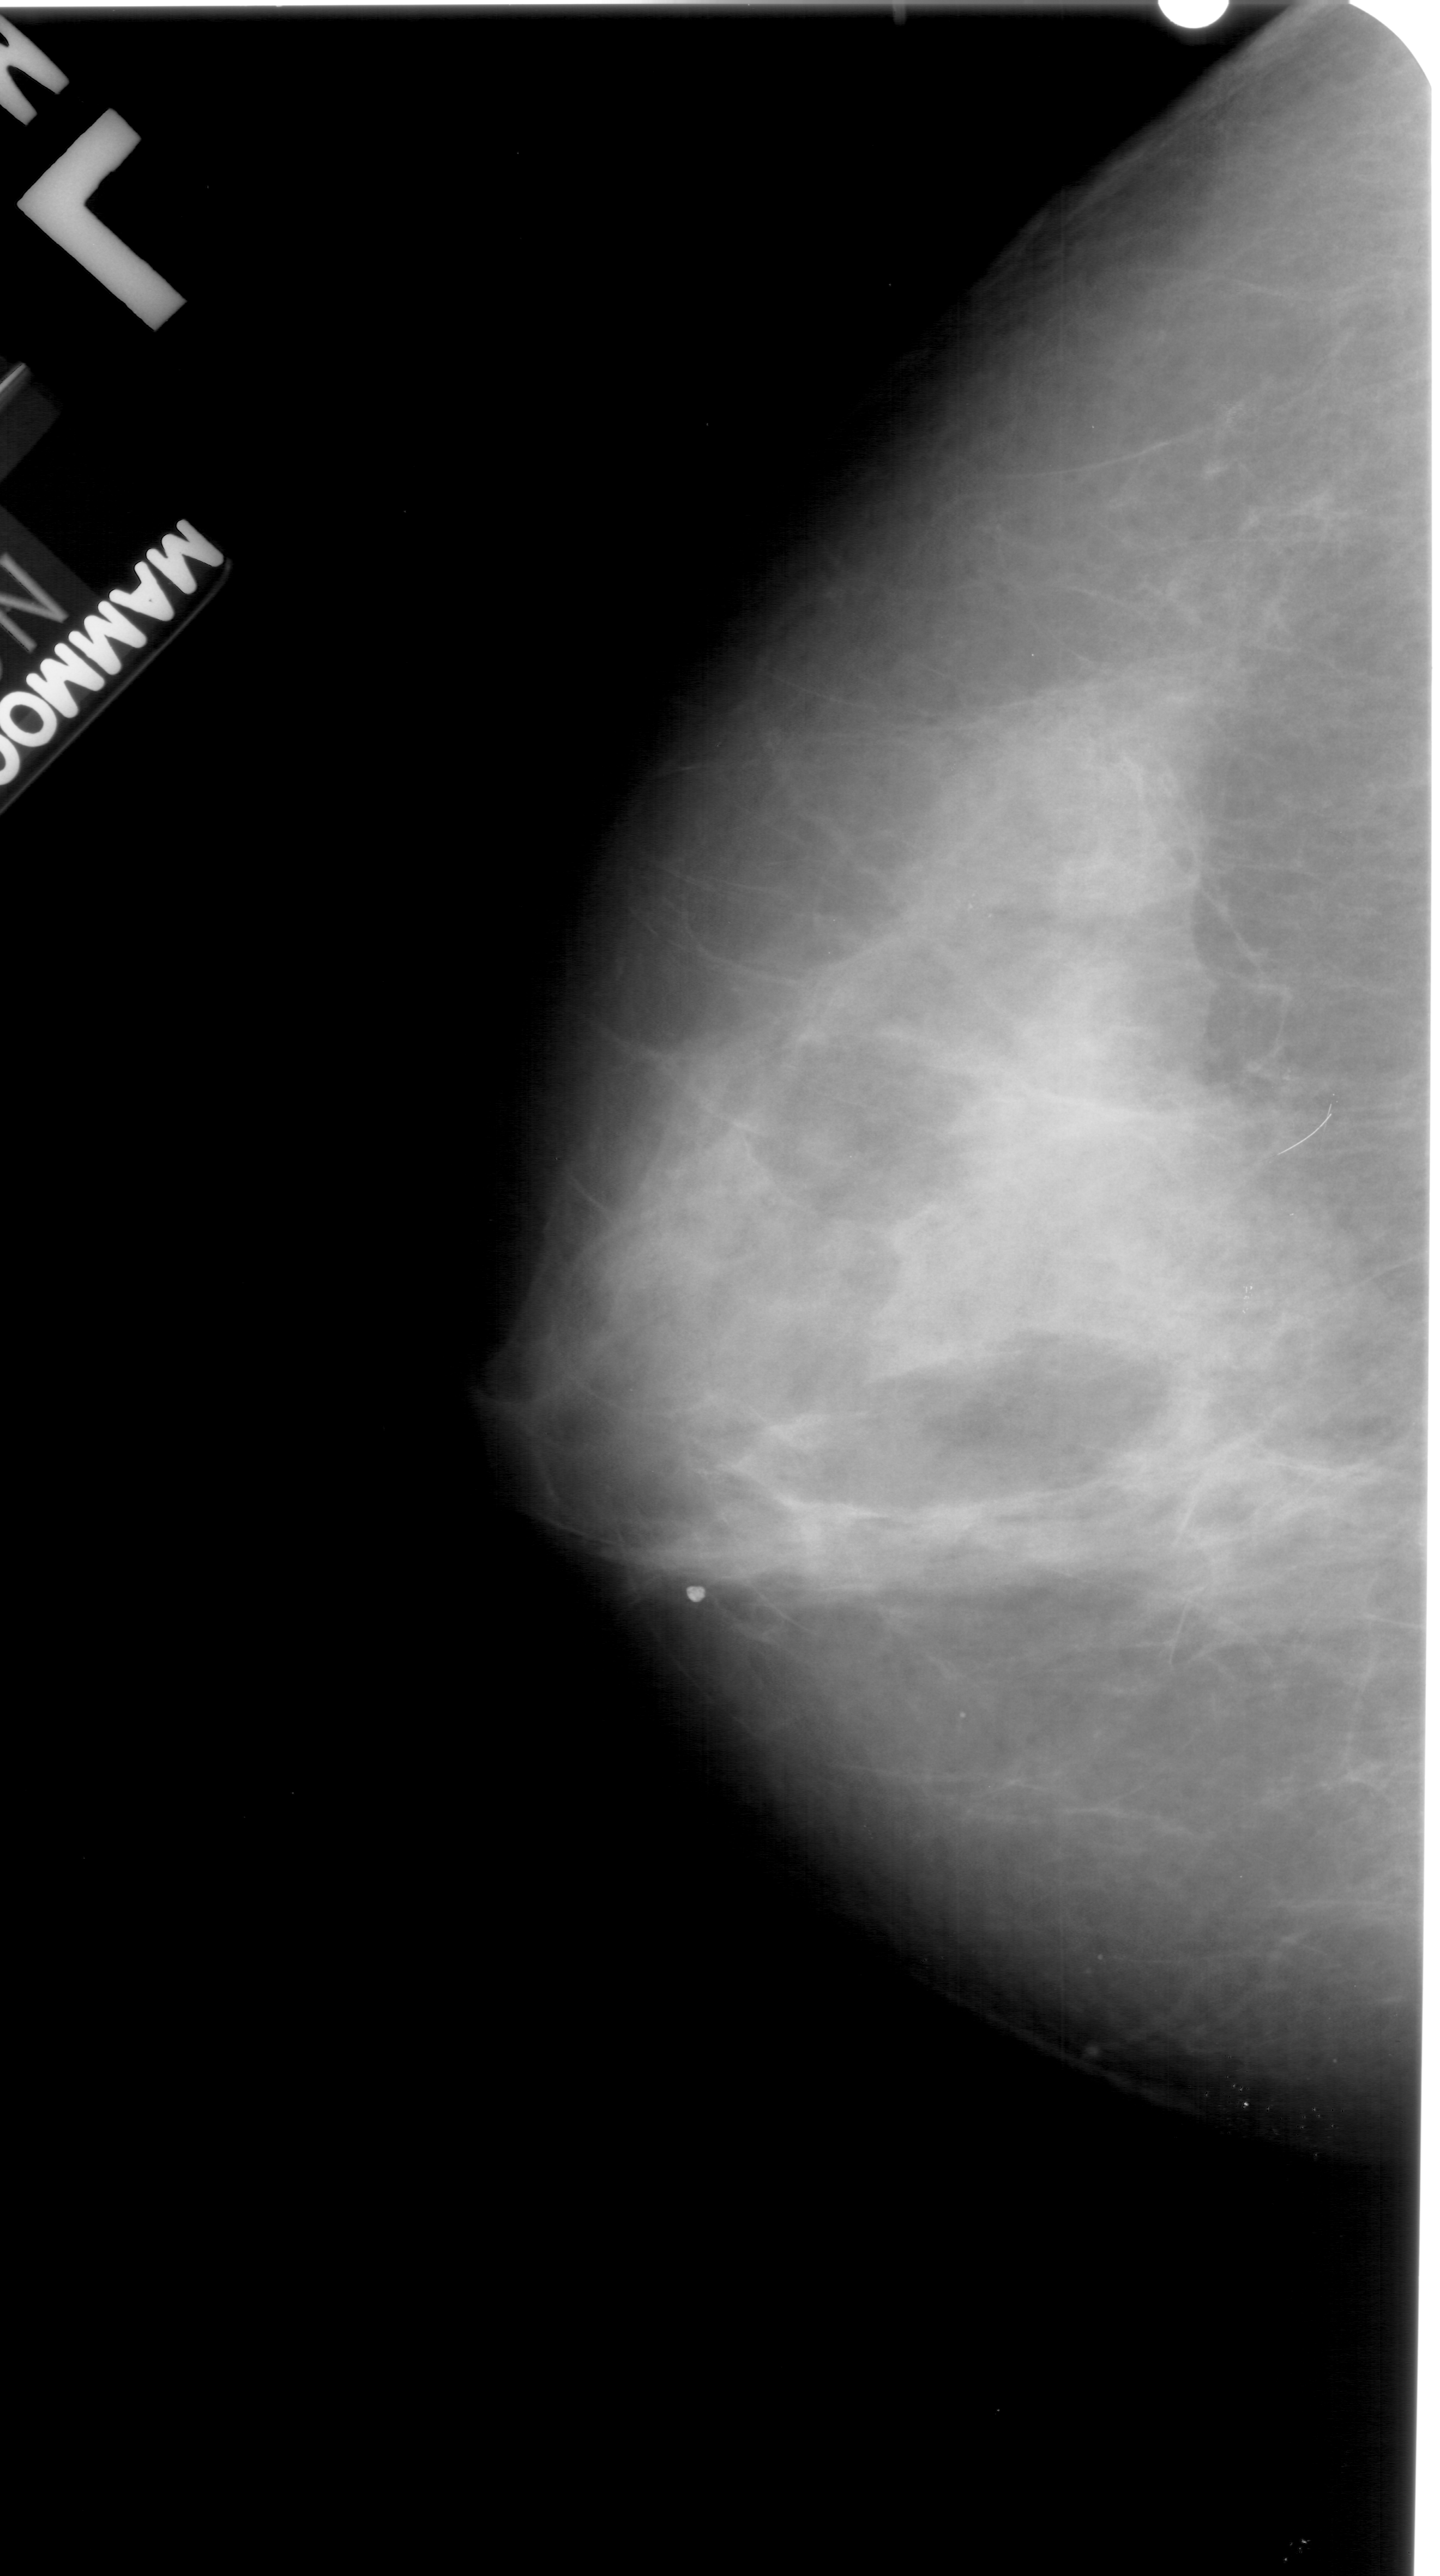
Mammogram (digitized film), left breast, craniocaudal (CC) view, breast composition: extremely dense (BI-RADS density category 4 of 4).
Finding: calcifications, morphology pleomorphic, distribution clustered; BI-RADS assessment category 4; pathology result (as recorded, not read from the image): benign.